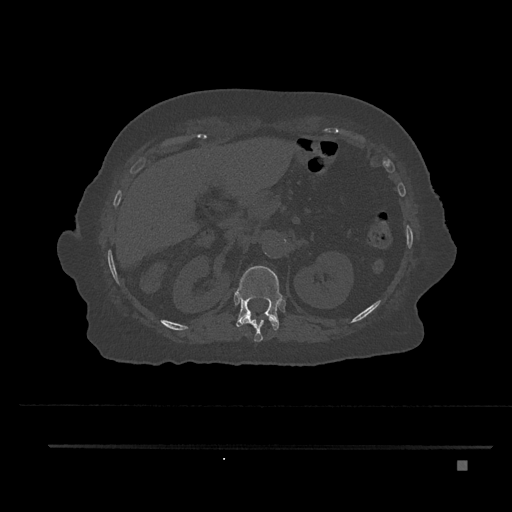
CT including the spine, one axial slice; slice 281 of 797 in the series (ordered by position); bone window (W 1800 / L 400 HU); 512 × 512 image matrix, field of view 437 × 437 mm. Female patient, age 76 years. From the clinical record (not read from this slice): primary cancer: lung; vertebrae with lytic lesions (as recorded): T11, L3.
Annotated regions visible in this slice (semi-automatic segmentation, software-assisted and operator-edited):
- T11 vertebra: bounding box <241,314,275,342> (left, top, right, bottom; pixels)
- T12 vertebra: <236,266,283,331>